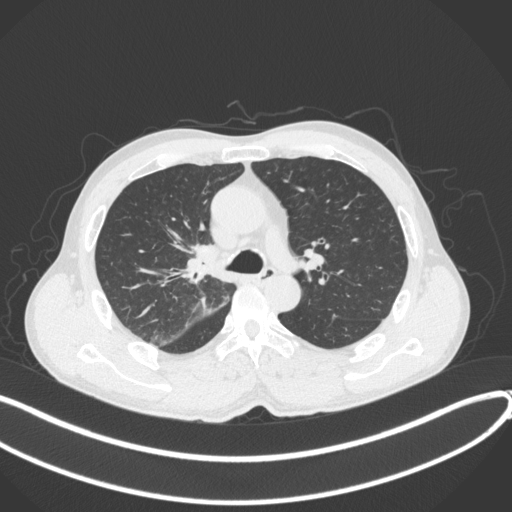
Chest CT, one axial slice; position 258 of 409 along the scan axis; 120 kVp; lung window (W 1500 / L -600 HU); 1 mm slice thickness; 512 × 512 image matrix. Patient: male, 53 years. Case-level facts recorded for this patient, not image findings: clinical TNM (as recorded): T1b N0 M0.
Structures marked on this image (bounding box drawn by a radiologist):
- lung tumour (recorded histology: squamous cell carcinoma): bounding box [x1, y1, x2, y2] px = [178, 240, 222, 282]